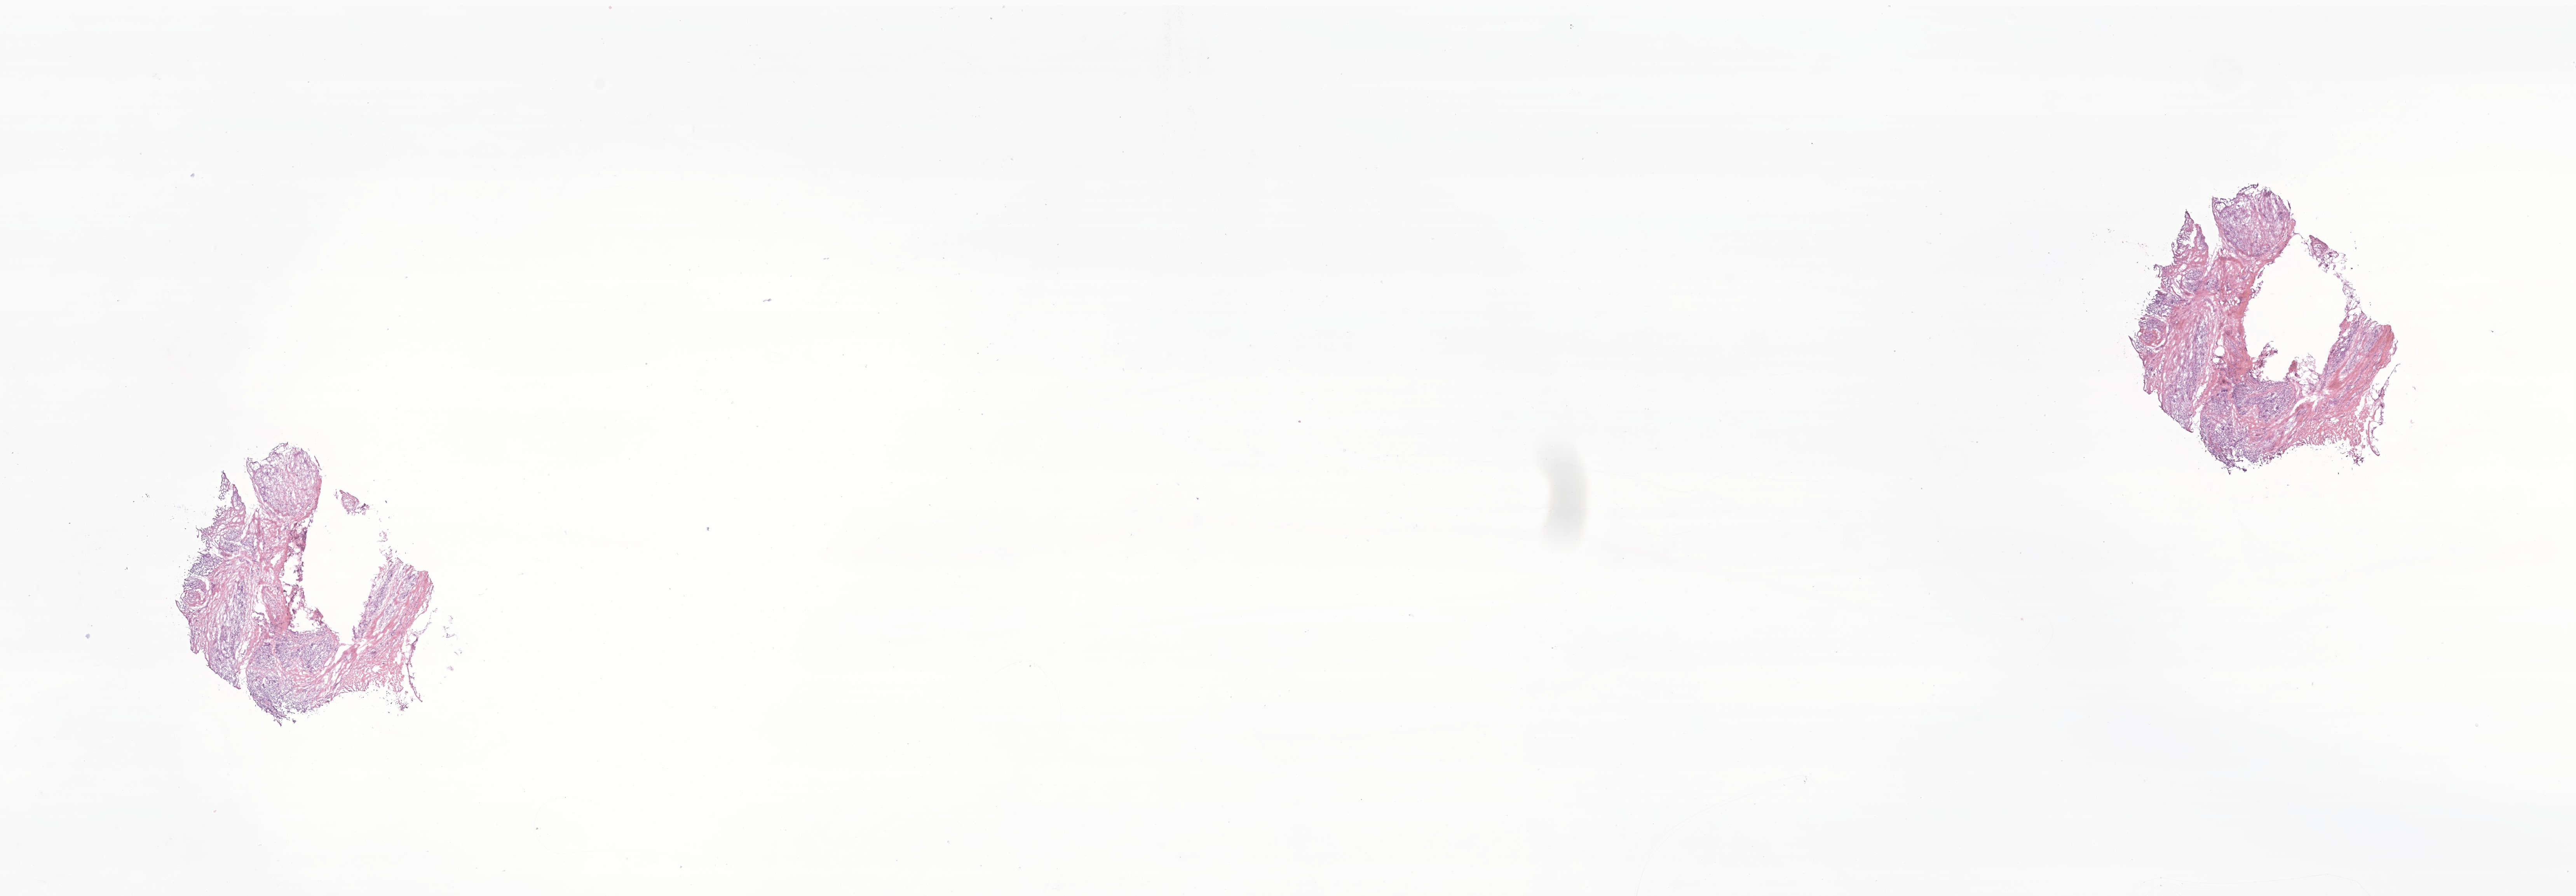
Whole-slide image, haematoxylin and eosin stain of tumor tissue from the upper limb lymph node — shown as a low-resolution overview of the whole scanned area (about 28.0 x 9.7 mm), frozen section (OCT-embedded). Patient: male, age 201 months (16 years 9 months).
Diagnosis (ICD-O-3 morphology term): Plexiform fibrohistiocytic tumor.